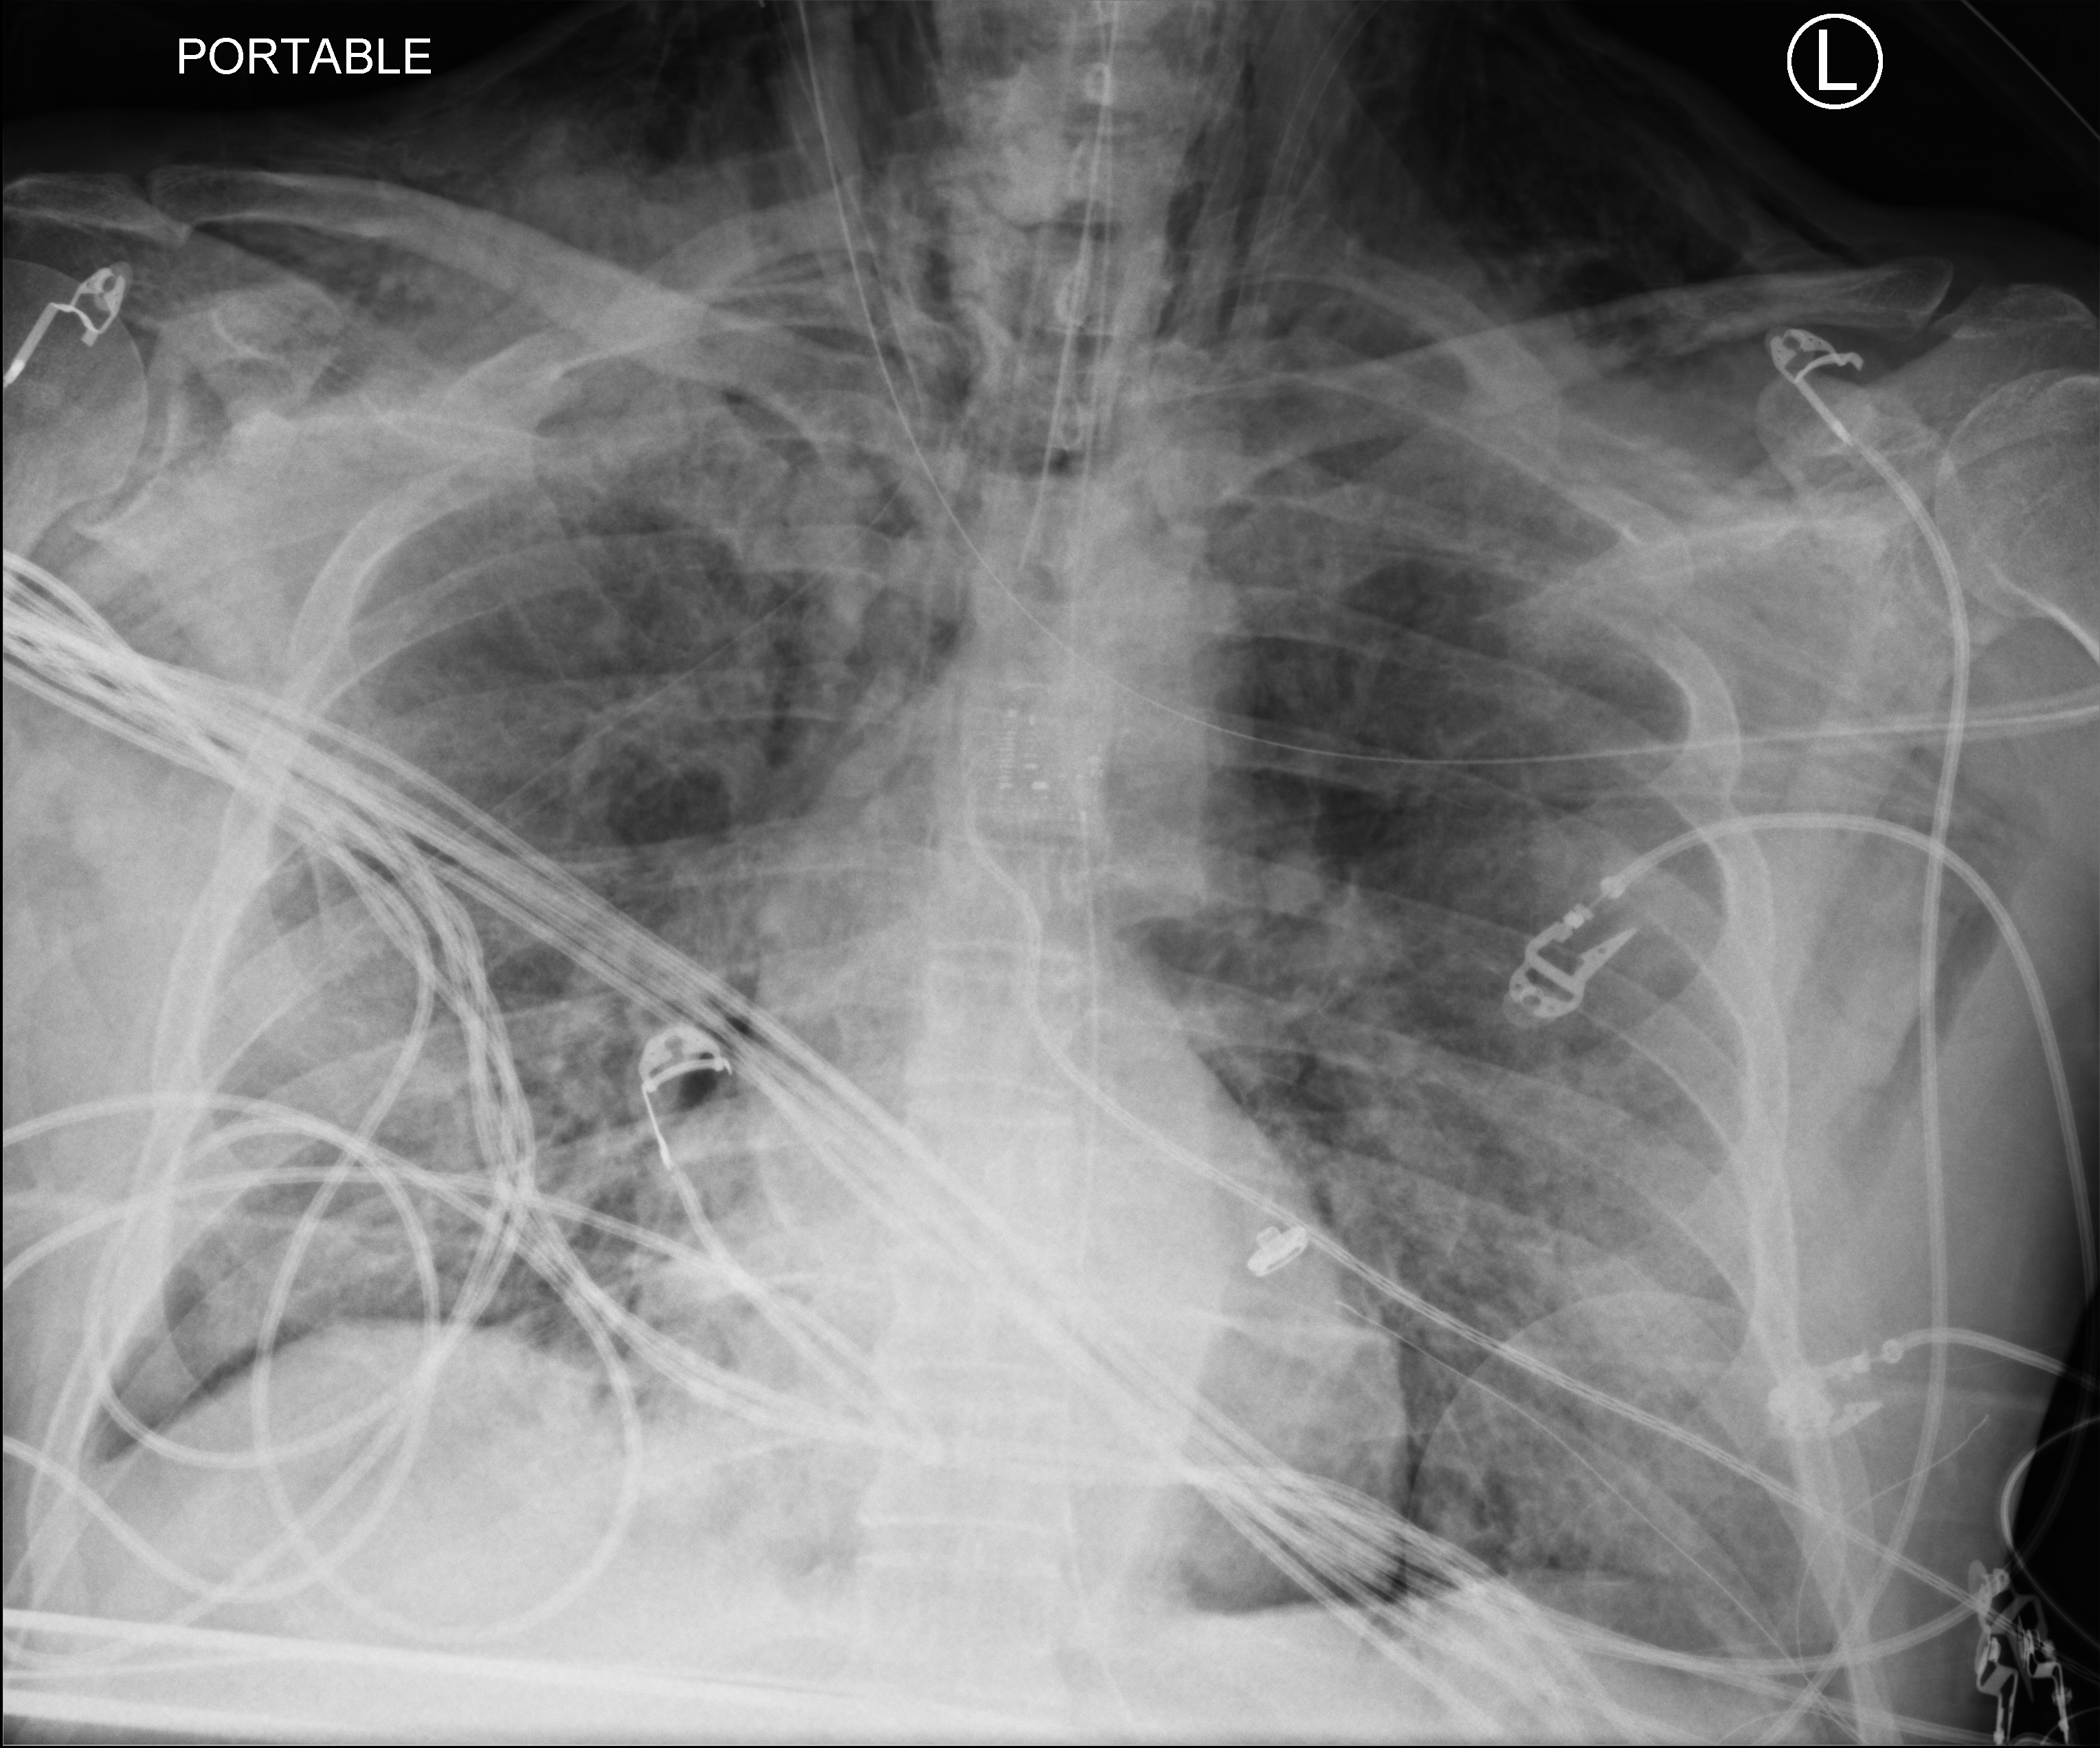
Bedside chest radiograph (computed radiography); anteroposterior (AP) projection. Male patient hospitalised with COVID-19, age 60–74 years.
Admission-level facts for this patient (not findings on this image; timing relative to this image not recorded): admitted to intensive care during this hospital stay: yes; smoking status (admission record): never.